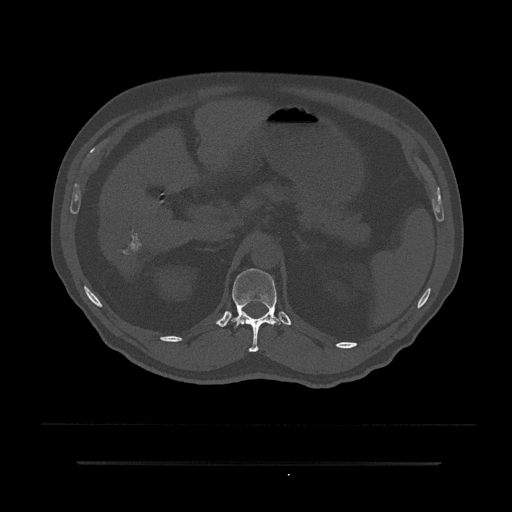
CT including the spine, one axial slice; slice 208 of 797 in the series (ordered by position); reconstruction kernel Br40s/3; bone window (W 1800 / L 400 HU); 512 × 512 image matrix, field of view 464 × 464 mm. Male patient, age 59 years. From the clinical record (not read from this slice): primary cancer: bile ducts.
Outlined on this slice (semi-automatically segmented with operator editing):
- T12 vertebra: box from (x=231, y=268) to (x=282, y=352) px